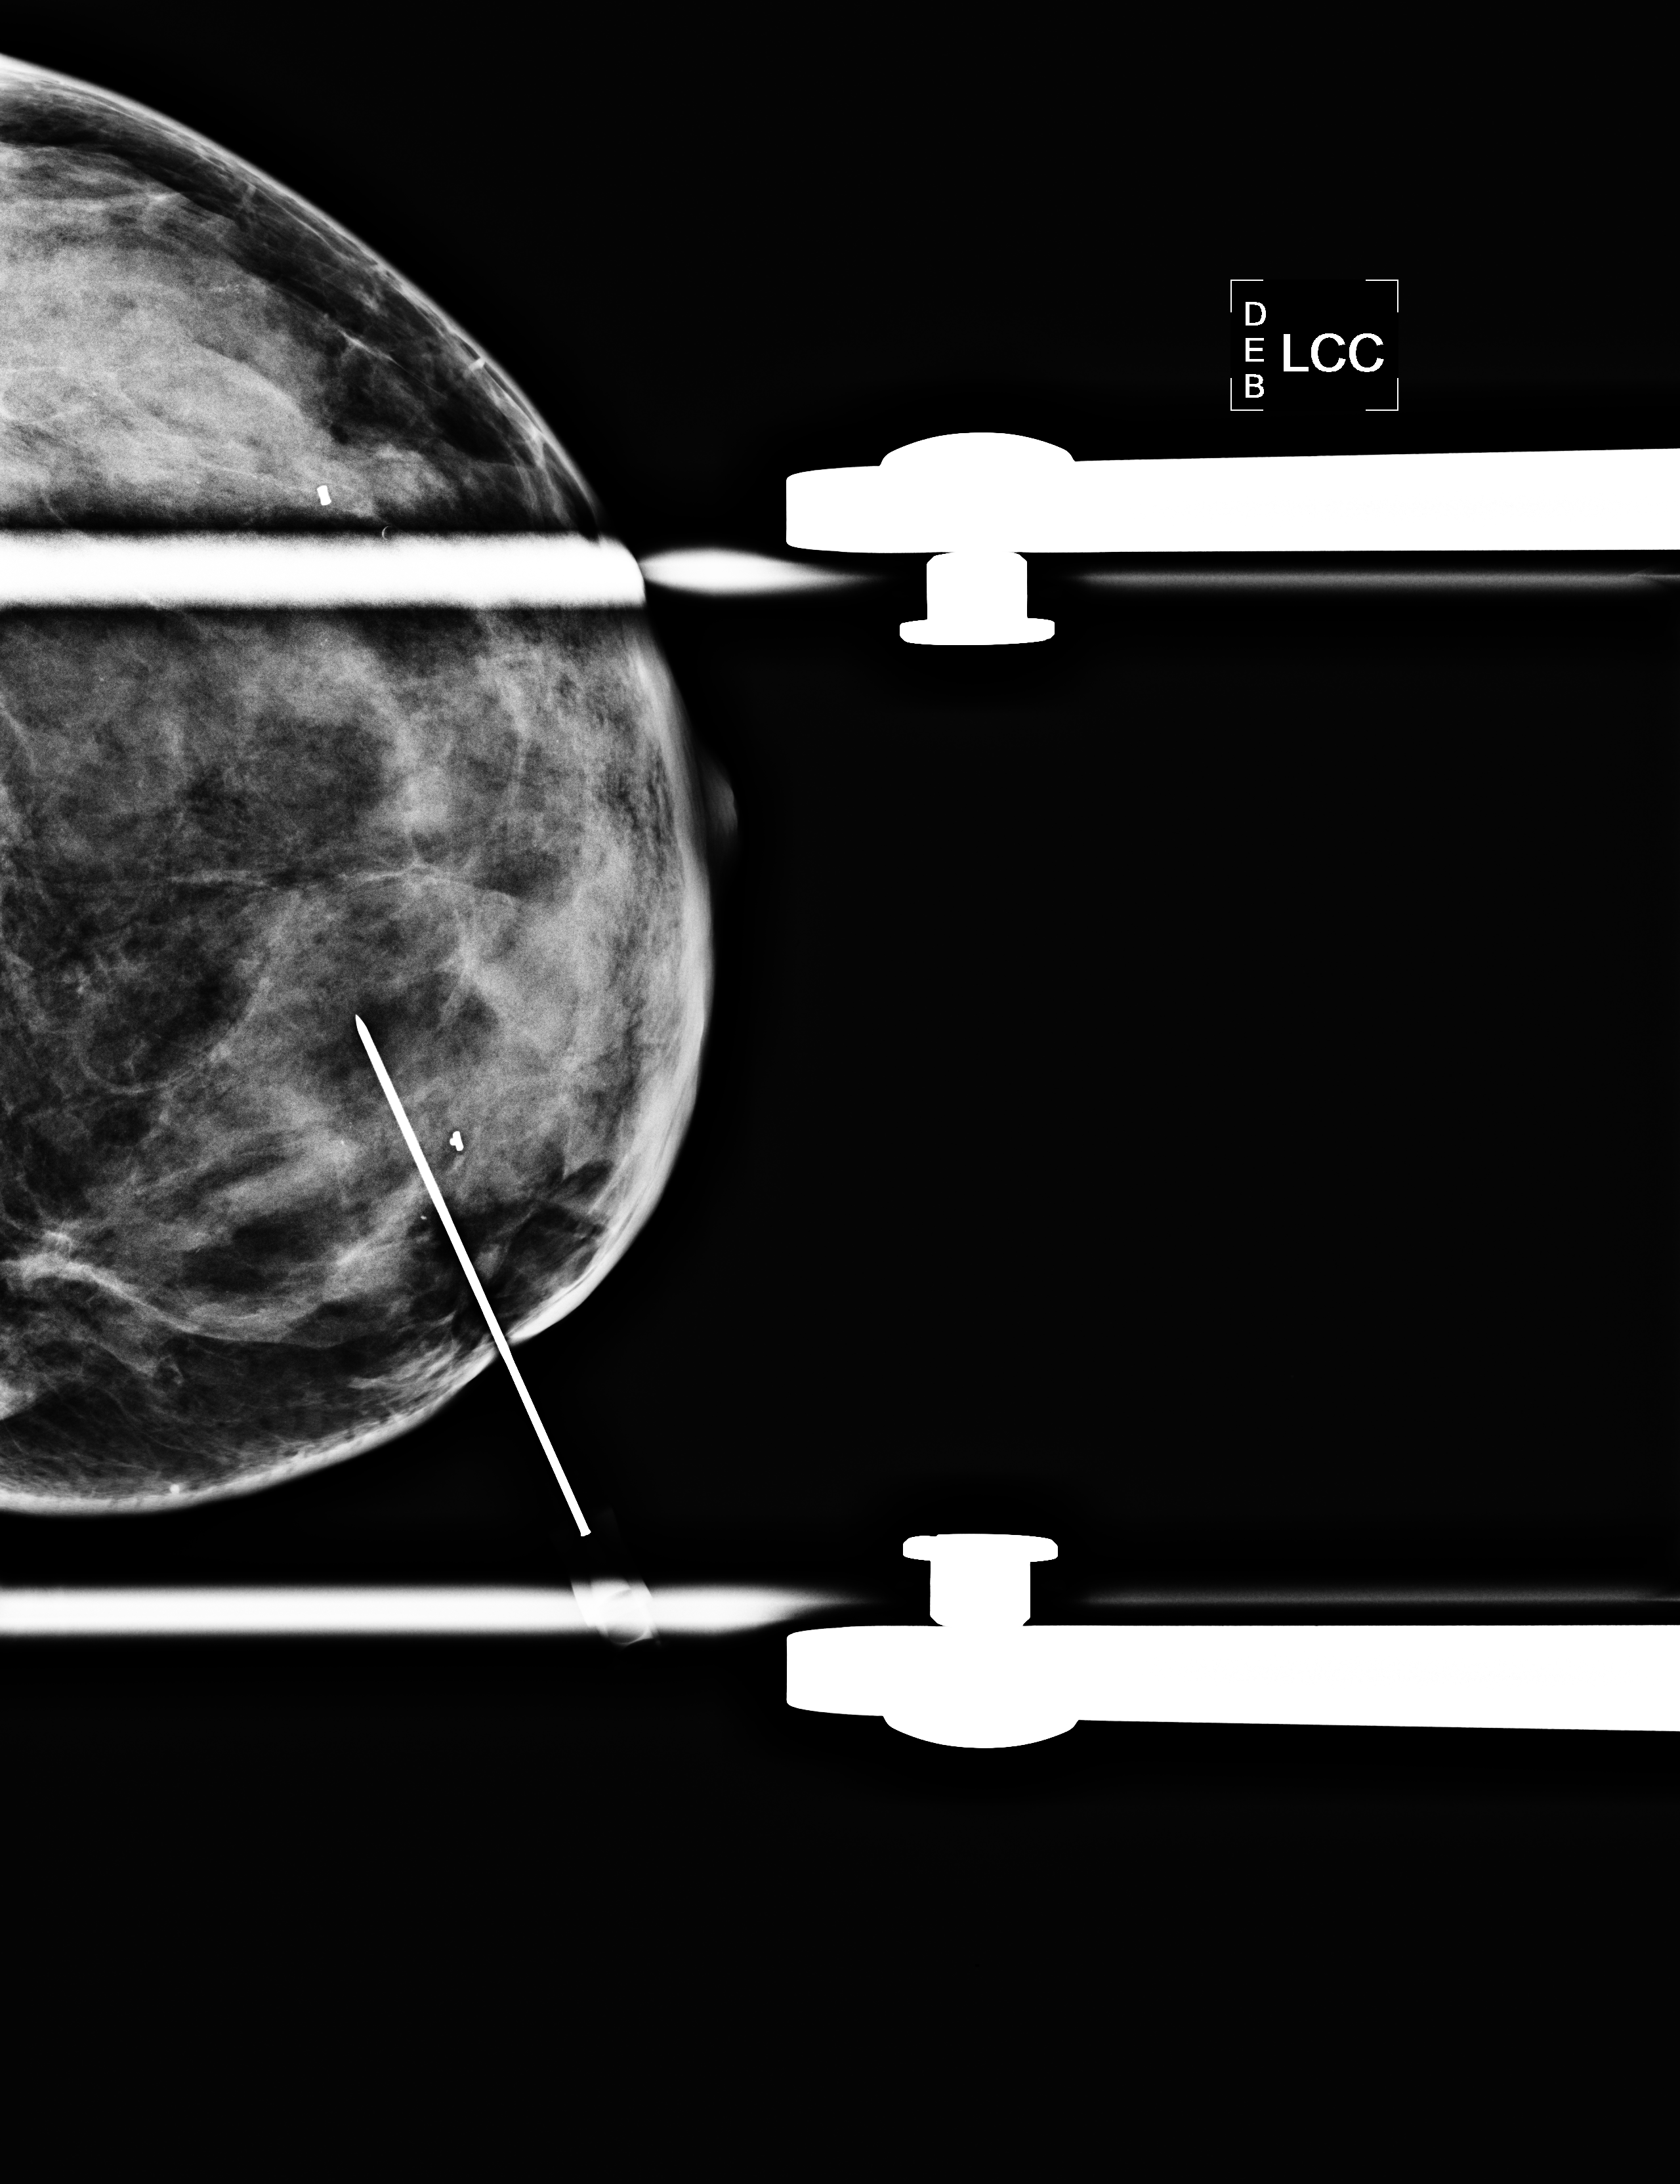
Needle-localisation mammographic view, left breast, CC view.
Patient-level pathology facts (clinical record, not image findings): pathology diagnosis: ducta CA in situ (left breast); receptor status (as recorded): ER neg, PR neg, HER2 pos.